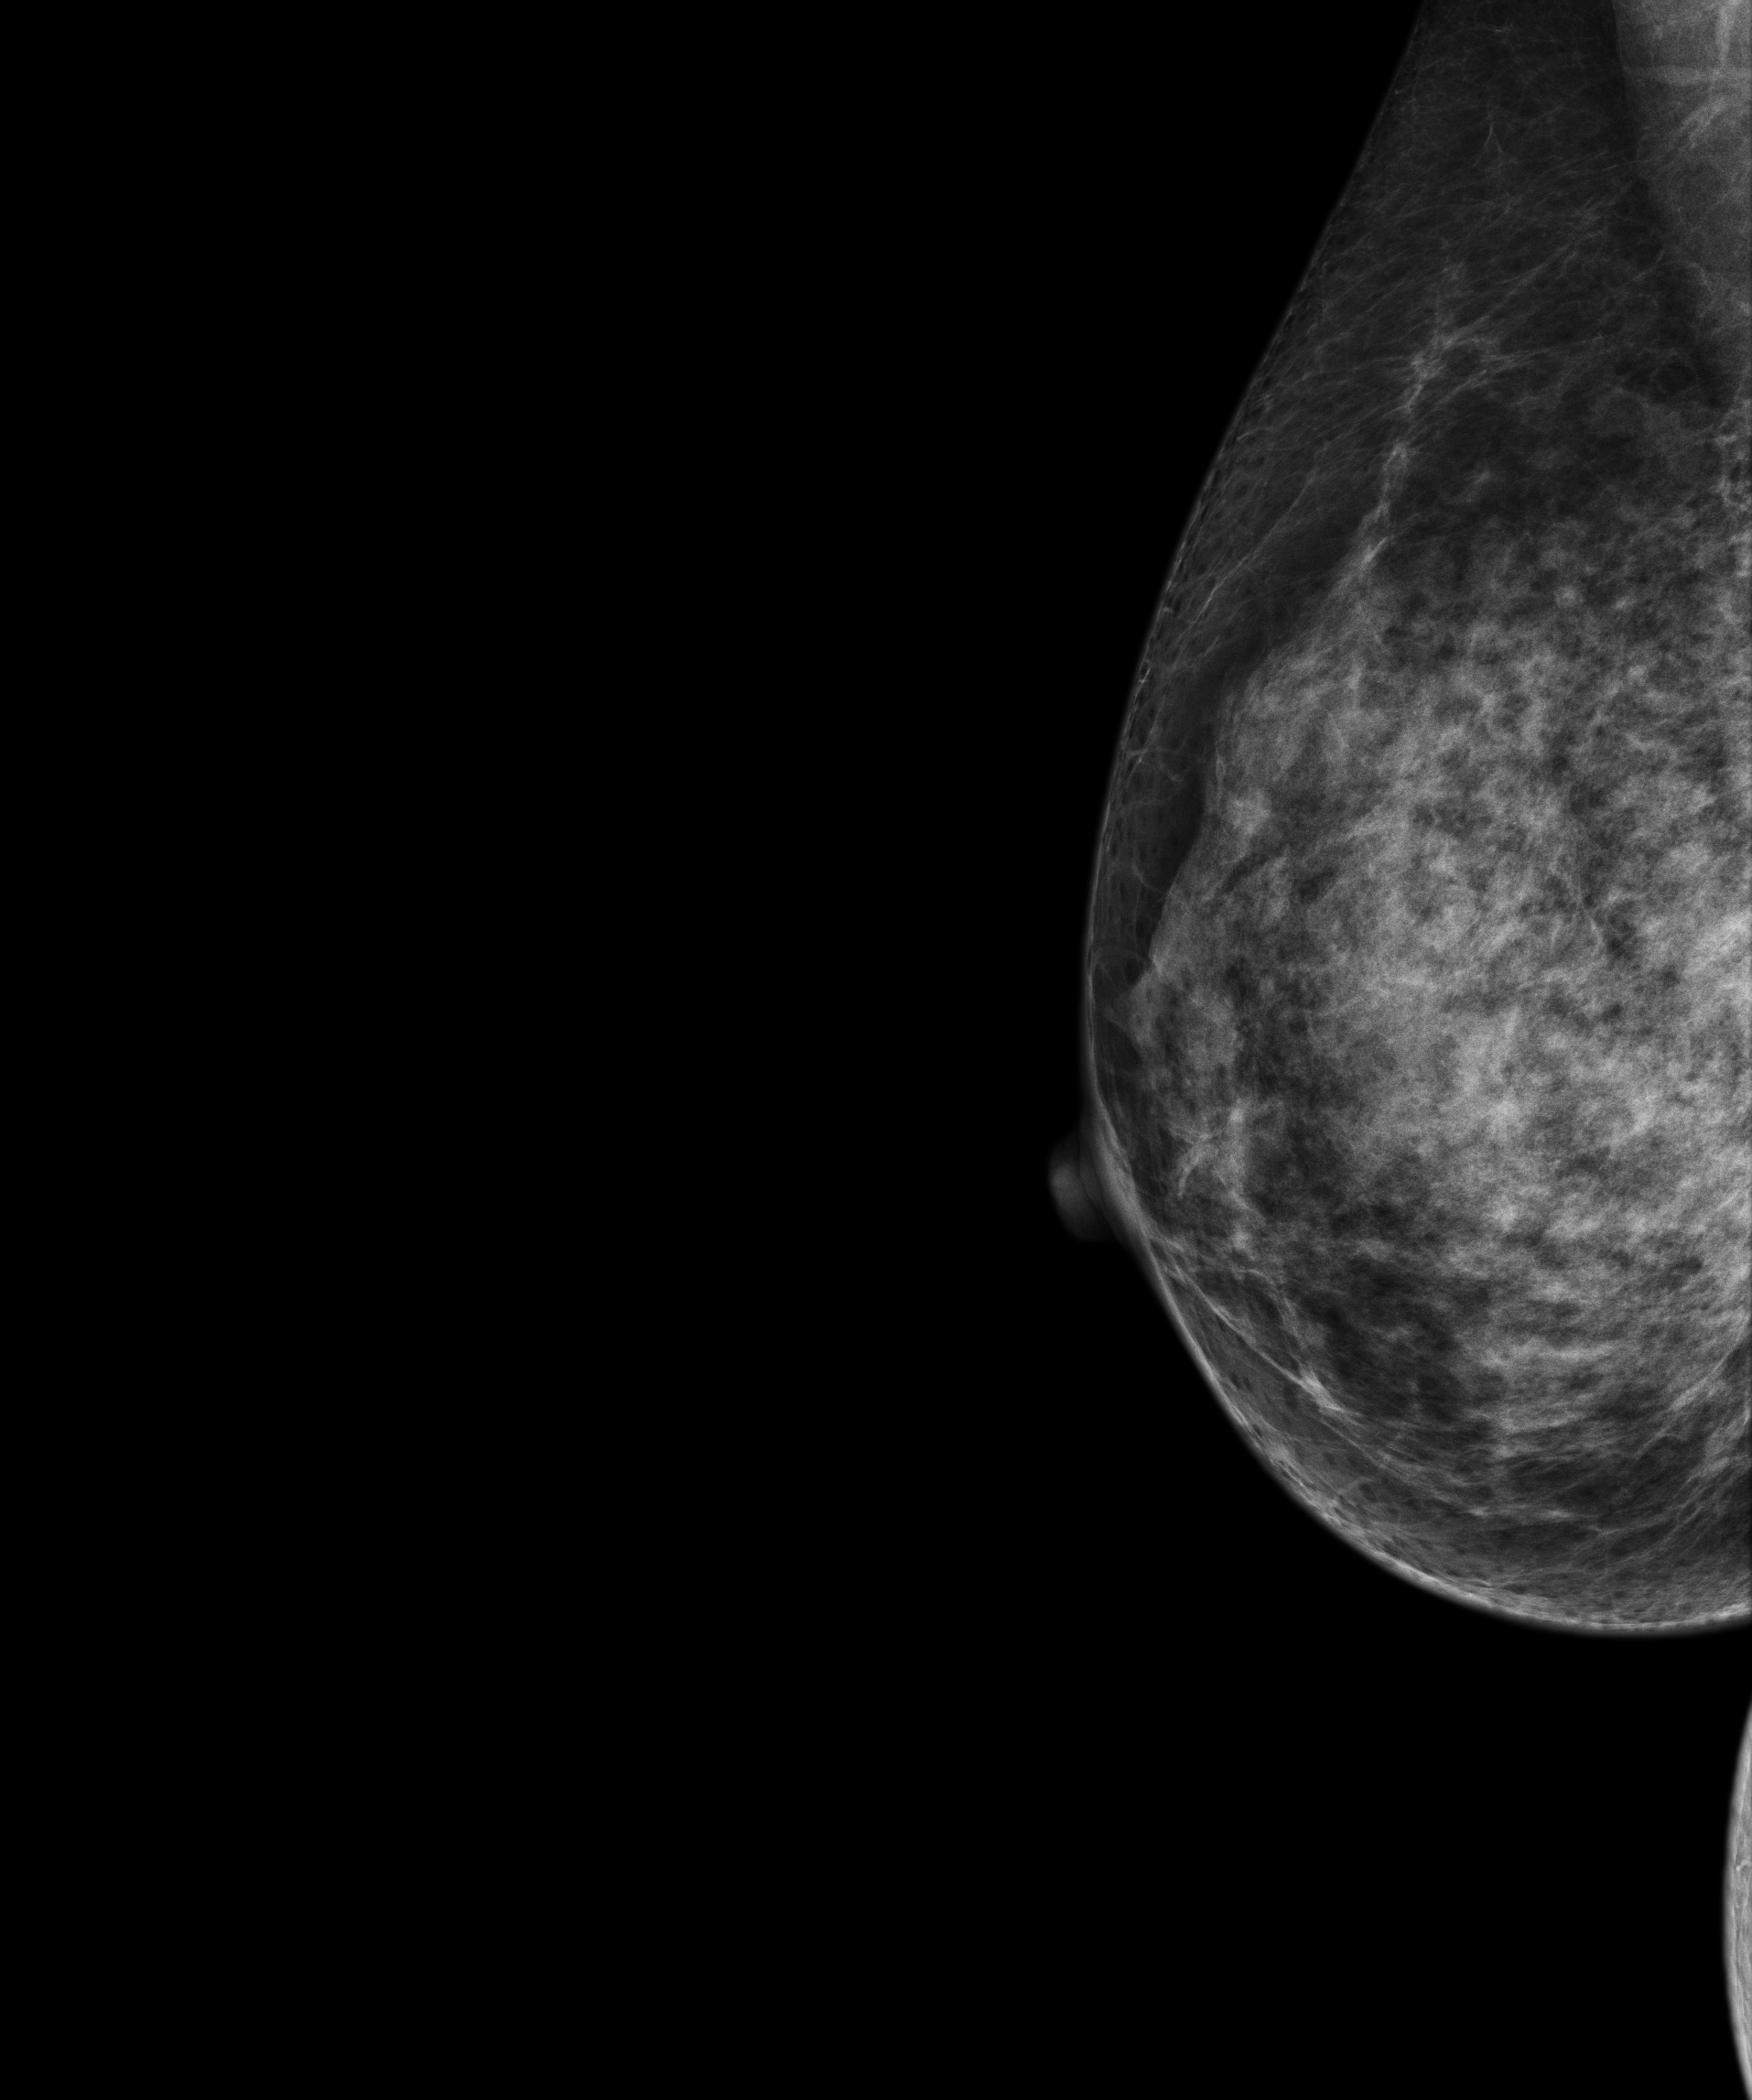
Annual screening mammography examination. Female patient, age 60 years.
Image type: full-field digital mammogram. Breast: right. Projection: laterally exaggerated craniocaudal (XCCL) view. BI-RADS breast density category at the screening exam (both breasts, scale 1–4): 4. Final BI-RADS assessment for this screening round (tomosynthesis exam, both breasts): category 1. Recall: no recall after this screen.